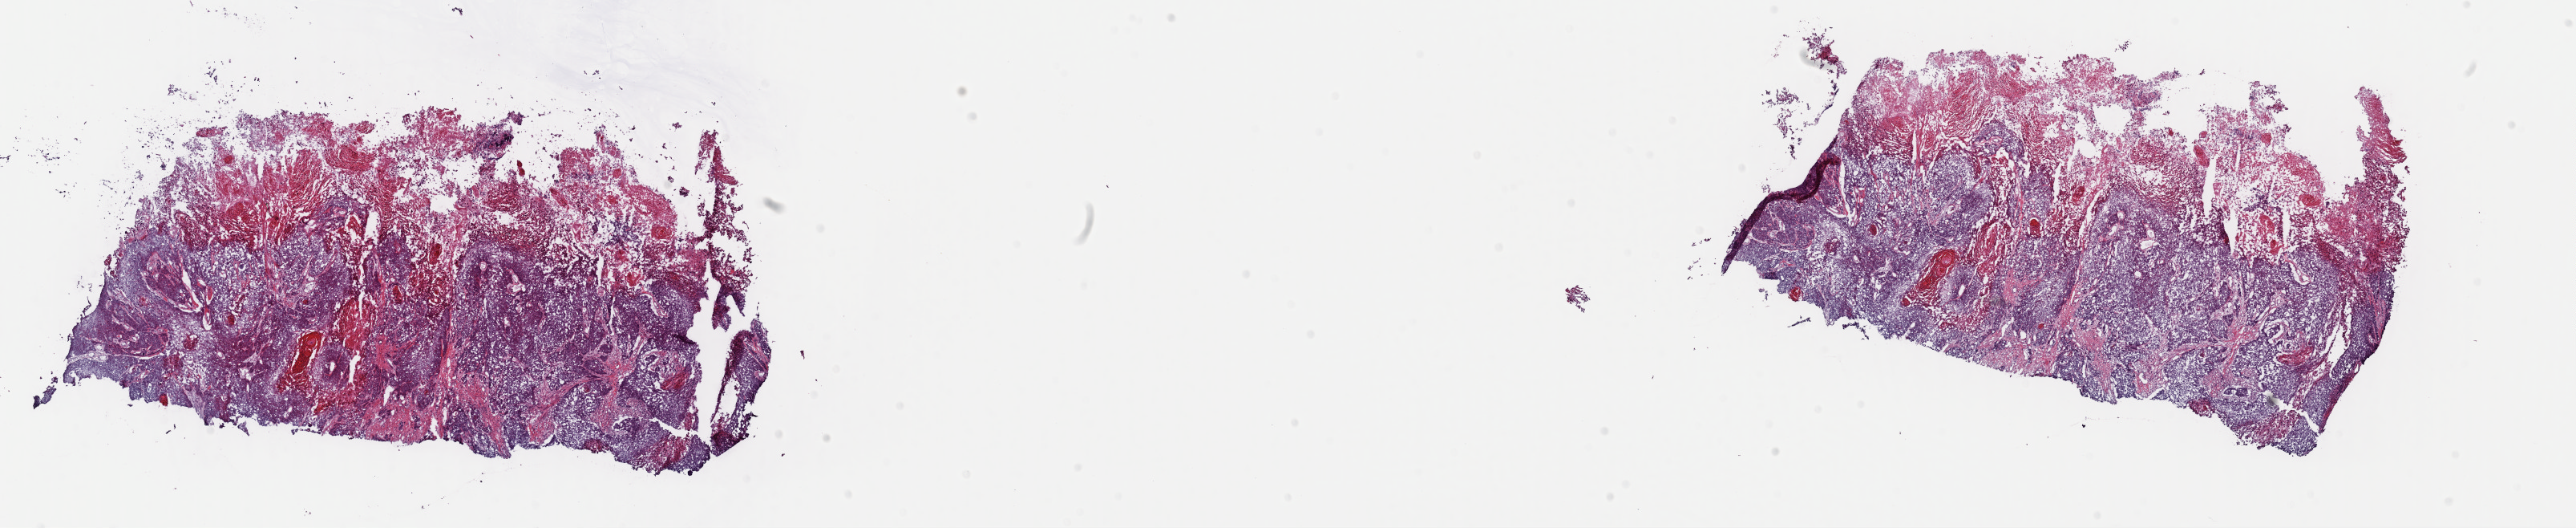
Digitized H&E-stained tissue section (whole slide) — whole scanned area (about 25.4 x 5.2 mm, acquisition: 40x scan) shown as a low-resolution overview, frozen section, sample: primary tumour, bladder. Male patient; age at initial diagnosis 76 years. Histologic grade: high grade. Slide review estimates, as recorded: tumour cells 75%, tumour nuclei 85%, normal cells 5%, stromal cells 0%, necrosis 20%. Inflammatory infiltration, as recorded: lymphocyte infiltration 1%, monocyte infiltration 1%, neutrophil infiltration 2%.
• AJCC pathologic stage: III (6th edition)
• diagnosis: Transitional cell carcinoma
• lymph nodes positive (case pathology): 0 of 8 examined